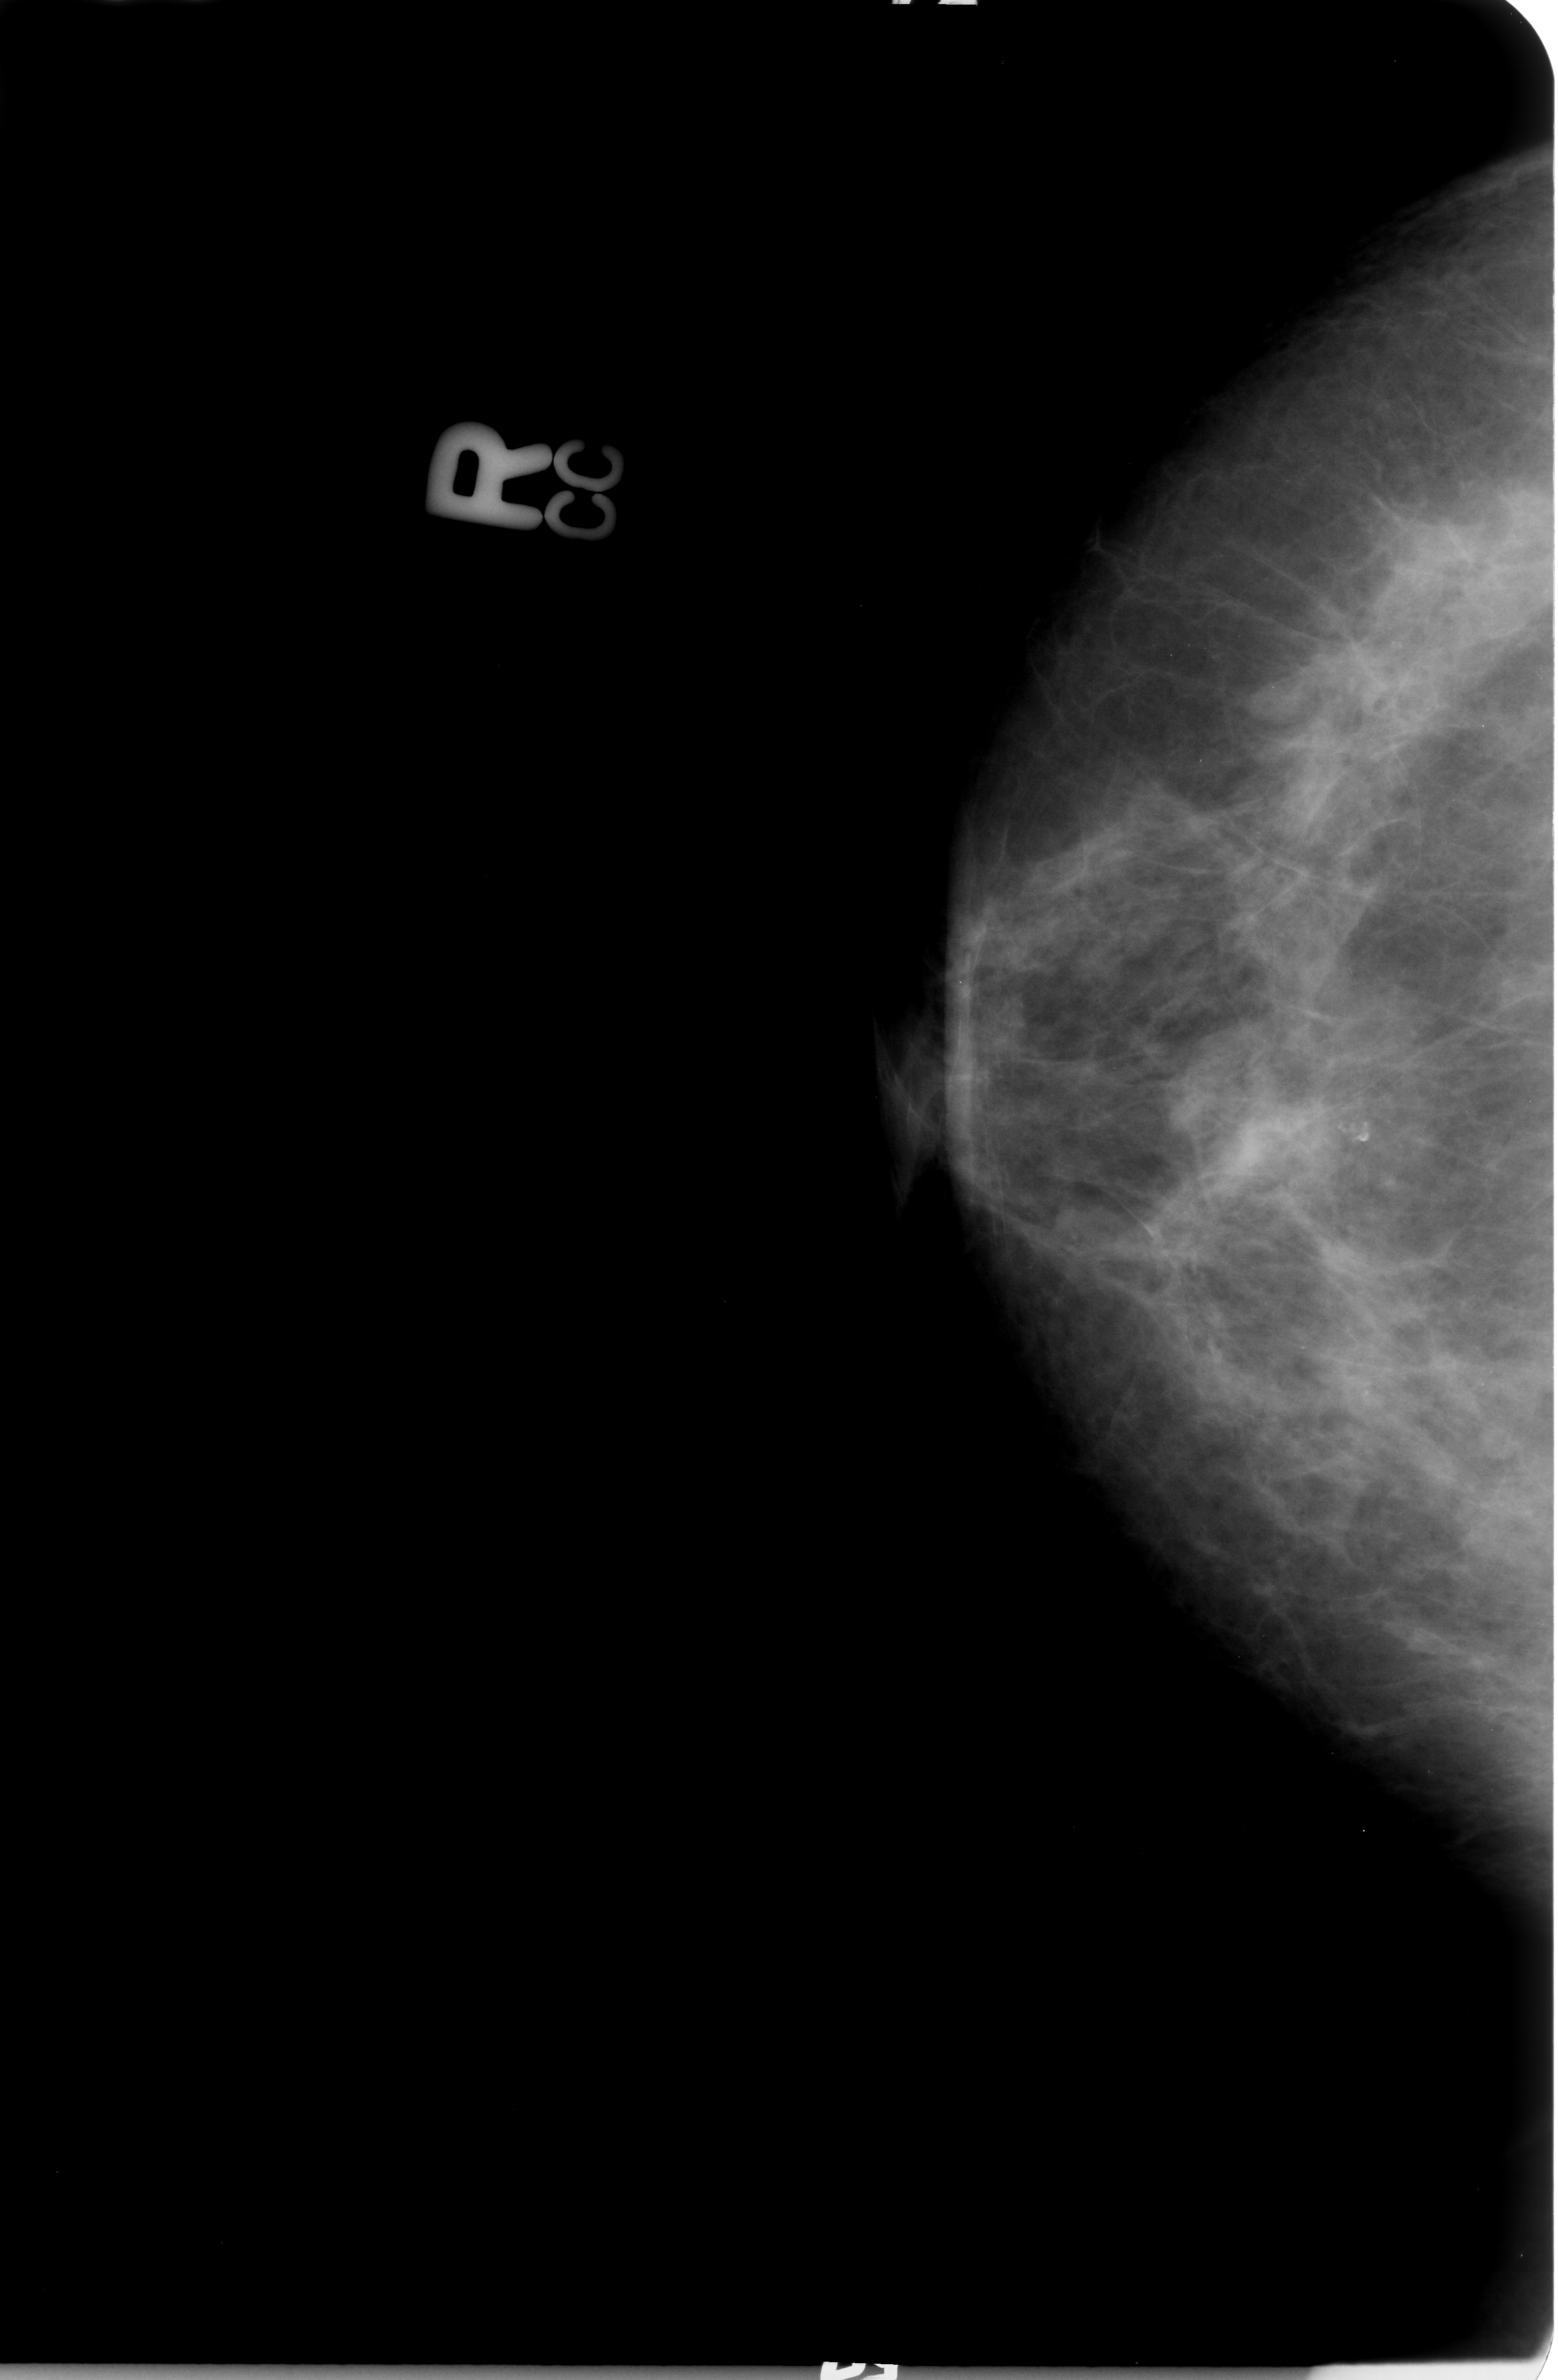
Mammogram (digitized film); right breast; CC view; breast composition: heterogeneously dense (BI-RADS density category 3 of 4).
- Marked findings (only marked abnormalities are described; nothing is implied about the rest of the image): Finding 1 of 2: mass, shape architectural distortion; BI-RADS assessment category 2; pathology (as recorded): benign.
- Finding 2 of 2: mass, shape architectural distortion; BI-RADS assessment category 2; pathology (as recorded): benign.